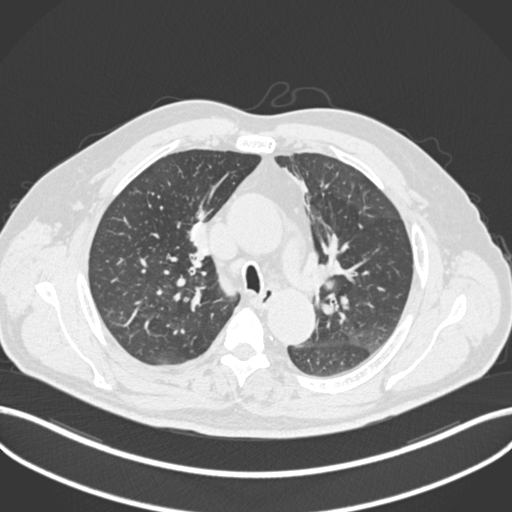
Chest CT, one axial slice. Reconstruction kernel B30f. 120 kVp. Lung window (W 1500 / L -600 HU). 512 × 512 image matrix, field of view 400 × 400 mm. Male patient, age 60 years. From the clinical record (not read from this slice): clinical TNM (as recorded): T1b N1 M0.
Structures marked on this image (bounding box drawn by a radiologist):
- lung tumour (recorded histology: squamous cell carcinoma): bounding box [x1, y1, x2, y2] px = [183, 209, 213, 269]